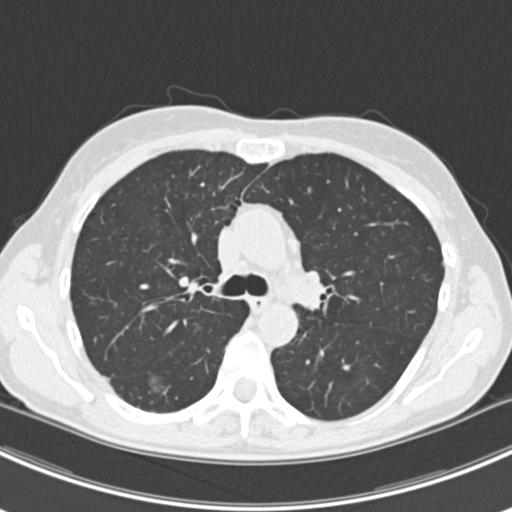
Low-dose screening chest CT, axial slice; baseline annual screen; lung window (W 1500 / L -600 HU); standard (soft-tissue) reconstruction kernel (B30f). Female, age 63 years at enrolment. Current smoker at enrolment.
- Lesion marked by an expert reader, bounding box <135,365,177,402> (left, top, right, bottom; pixels).
- The screening reader recorded 10 non-calcified nodules or masses ≥4 mm on this exam (right lower lobe, right lower lobe, left lower lobe, left lower lobe, right middle lobe, right lower lobe, left lower lobe, left upper lobe, right upper lobe, left upper lobe); which of them this box marks is not recorded.
- Official screen result: positive, change unspecified: nodule(s) >= 4 mm or enlarging nodule(s), mass(es), or other non-specific abnormalities suspicious for lung cancer.